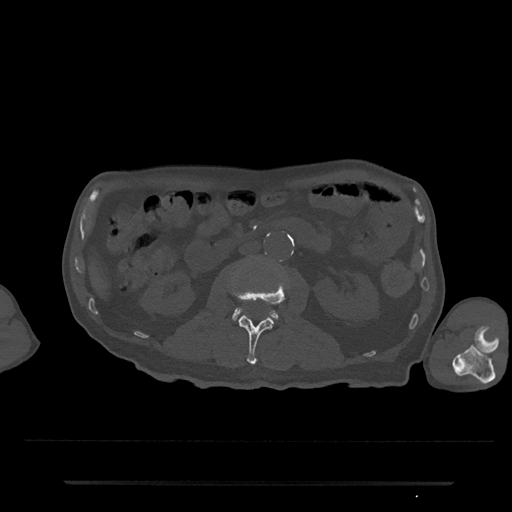
CT including the spine, one axial slice; slice 36 of 797 in the series (ordered by position); 120 kVp; bone window (W 1800 / L 400 HU); 0.5 mm slice thickness; 512 × 512 image matrix, field of view 427 × 427 mm. Patient: male, 74 years. Case-level facts recorded for this patient, not image findings: primary cancer: prostate.
Structures marked on this image (semi-automatic segmentation, software-assisted and operator-edited):
- L2 vertebra: bounding box [x1, y1, x2, y2] px = [231, 279, 290, 365]
- L3 vertebra: [232, 307, 279, 321]